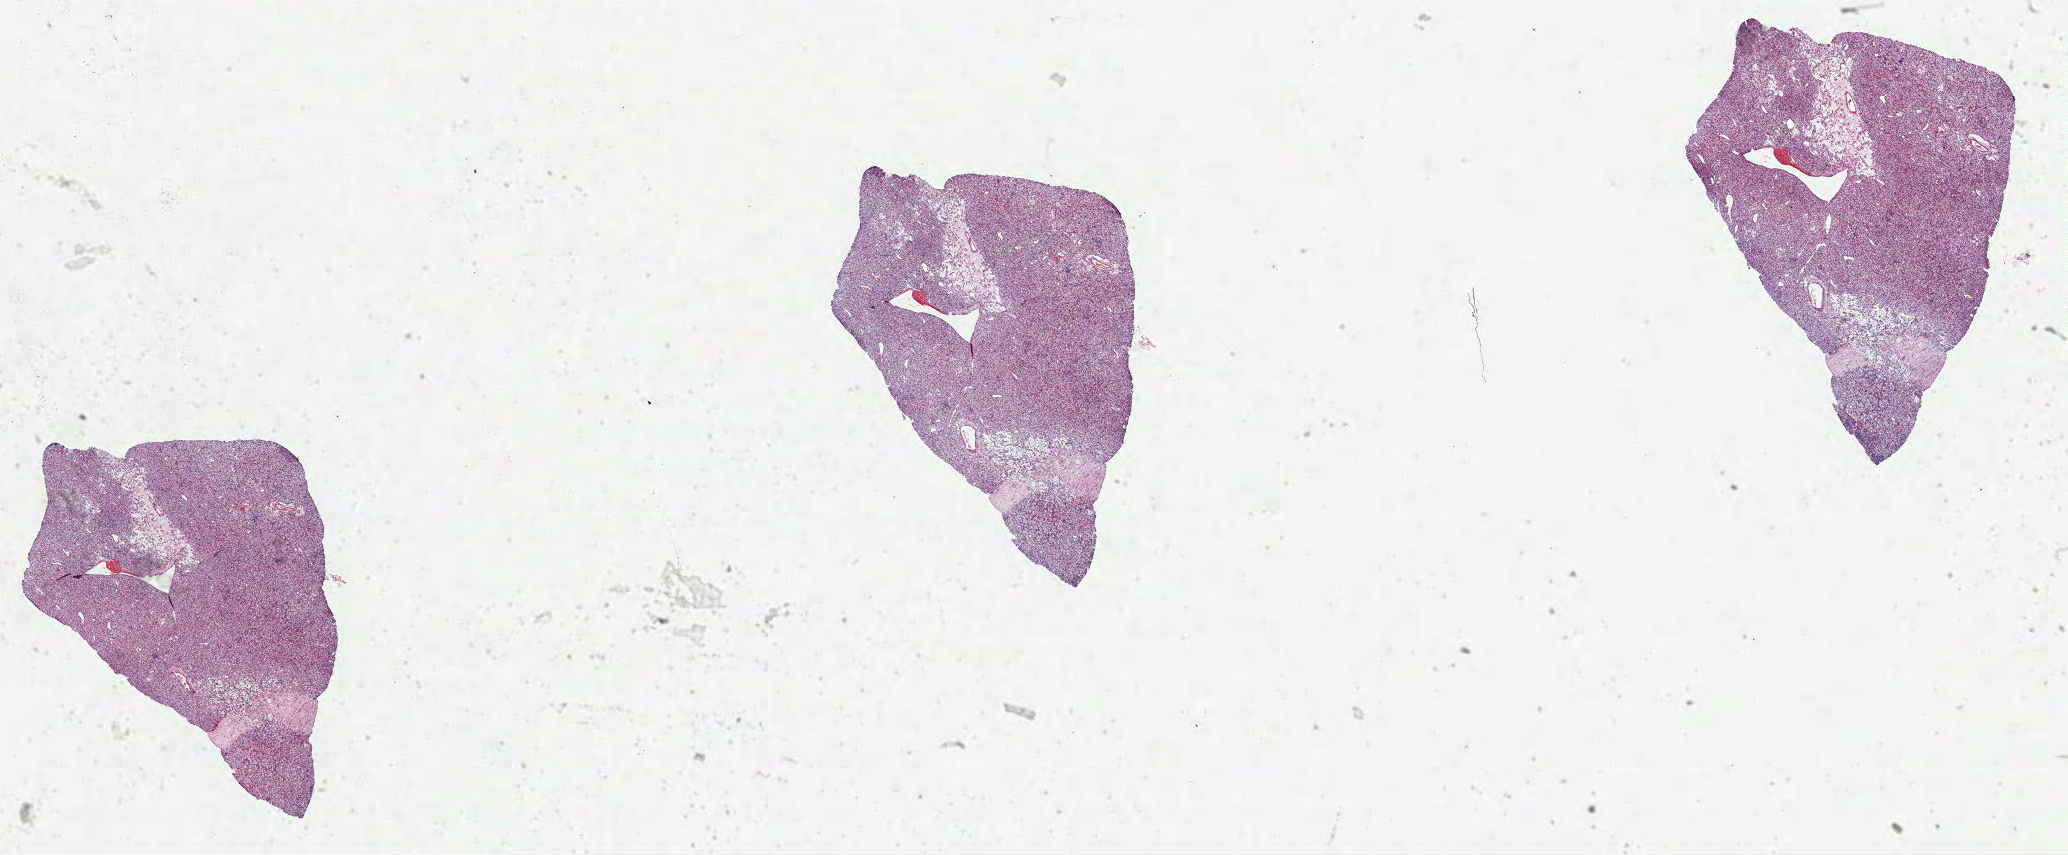
Hematoxylin and eosin (H&E) stained whole-slide image, whole scanned area (about 33.4 x 13.8 mm, acquisition: 40x scan) shown as a low-resolution overview; formalin-fixed paraffin-embedded (FFPE) diagnostic section; sample: primary tumour, kidney. Male patient; age at initial diagnosis 74 years.
Pathologic diagnosis: Clear cell adenocarcinoma, NOS.